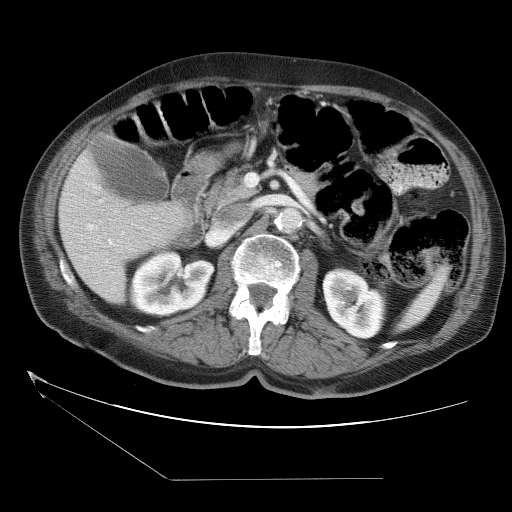
Contrast-enhanced abdominal CT (liver protocol), one axial slice; slice 13 of 38 in the series (ordered by position); one of 2 acquisitions stored at this slice position; soft-tissue window (W 400 / L 40 HU); 512 × 512 image matrix. From the clinical record (not read from this slice): diagnosis: hepatocellular carcinoma (patient treated with transarterial chemoembolisation; whether this scan precedes or follows treatment is not stated here); TNM stage (as recorded): Stage-II; Child-Pugh class: A; tumour nodularity: multinodular; tumour size: 0.8 cm.
Outlined on this slice (semi-automatically segmented with operator editing):
- liver parenchyma outside the tumour (the mass and vessels are separate outlines, so this box may not span the whole liver): box from (x=58, y=149) to (x=188, y=302) px
- liver vessels: (x=87, y=224)–(x=124, y=262)